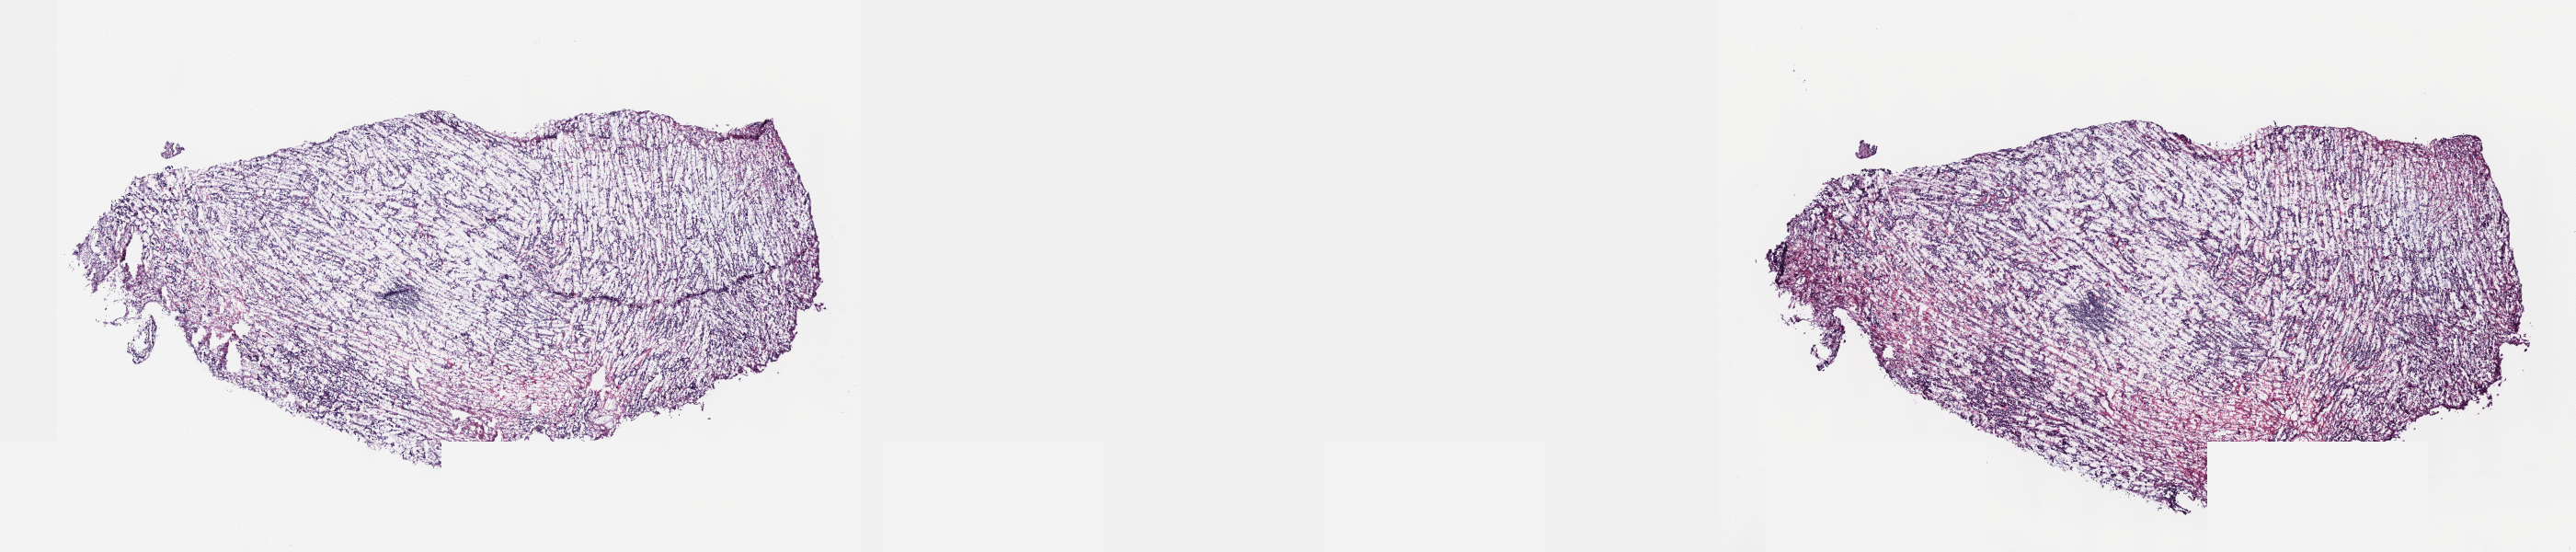
Whole-slide histology image, Hematoxylin and eosin (H&E) stained, low-resolution overview of the scanned area, about 22.6 x 4.8 mm. Frozen section. Sample: primary tumour, mesothelium. Patient: female, age at initial diagnosis 48 years. Slide review estimates, as recorded: tumour cells 100%, tumour nuclei 75%, normal cells 0%, stromal cells 0%, necrosis 0%. Infiltration values recorded for this section: lymphocyte infiltration 2%, monocyte infiltration 0%, neutrophil infiltration 0%.
- laterality: left
- diagnosis: Epithelioid mesothelioma, malignant
- TNM: T3 N1 MX
- AJCC pathologic stage: III (7th edition)